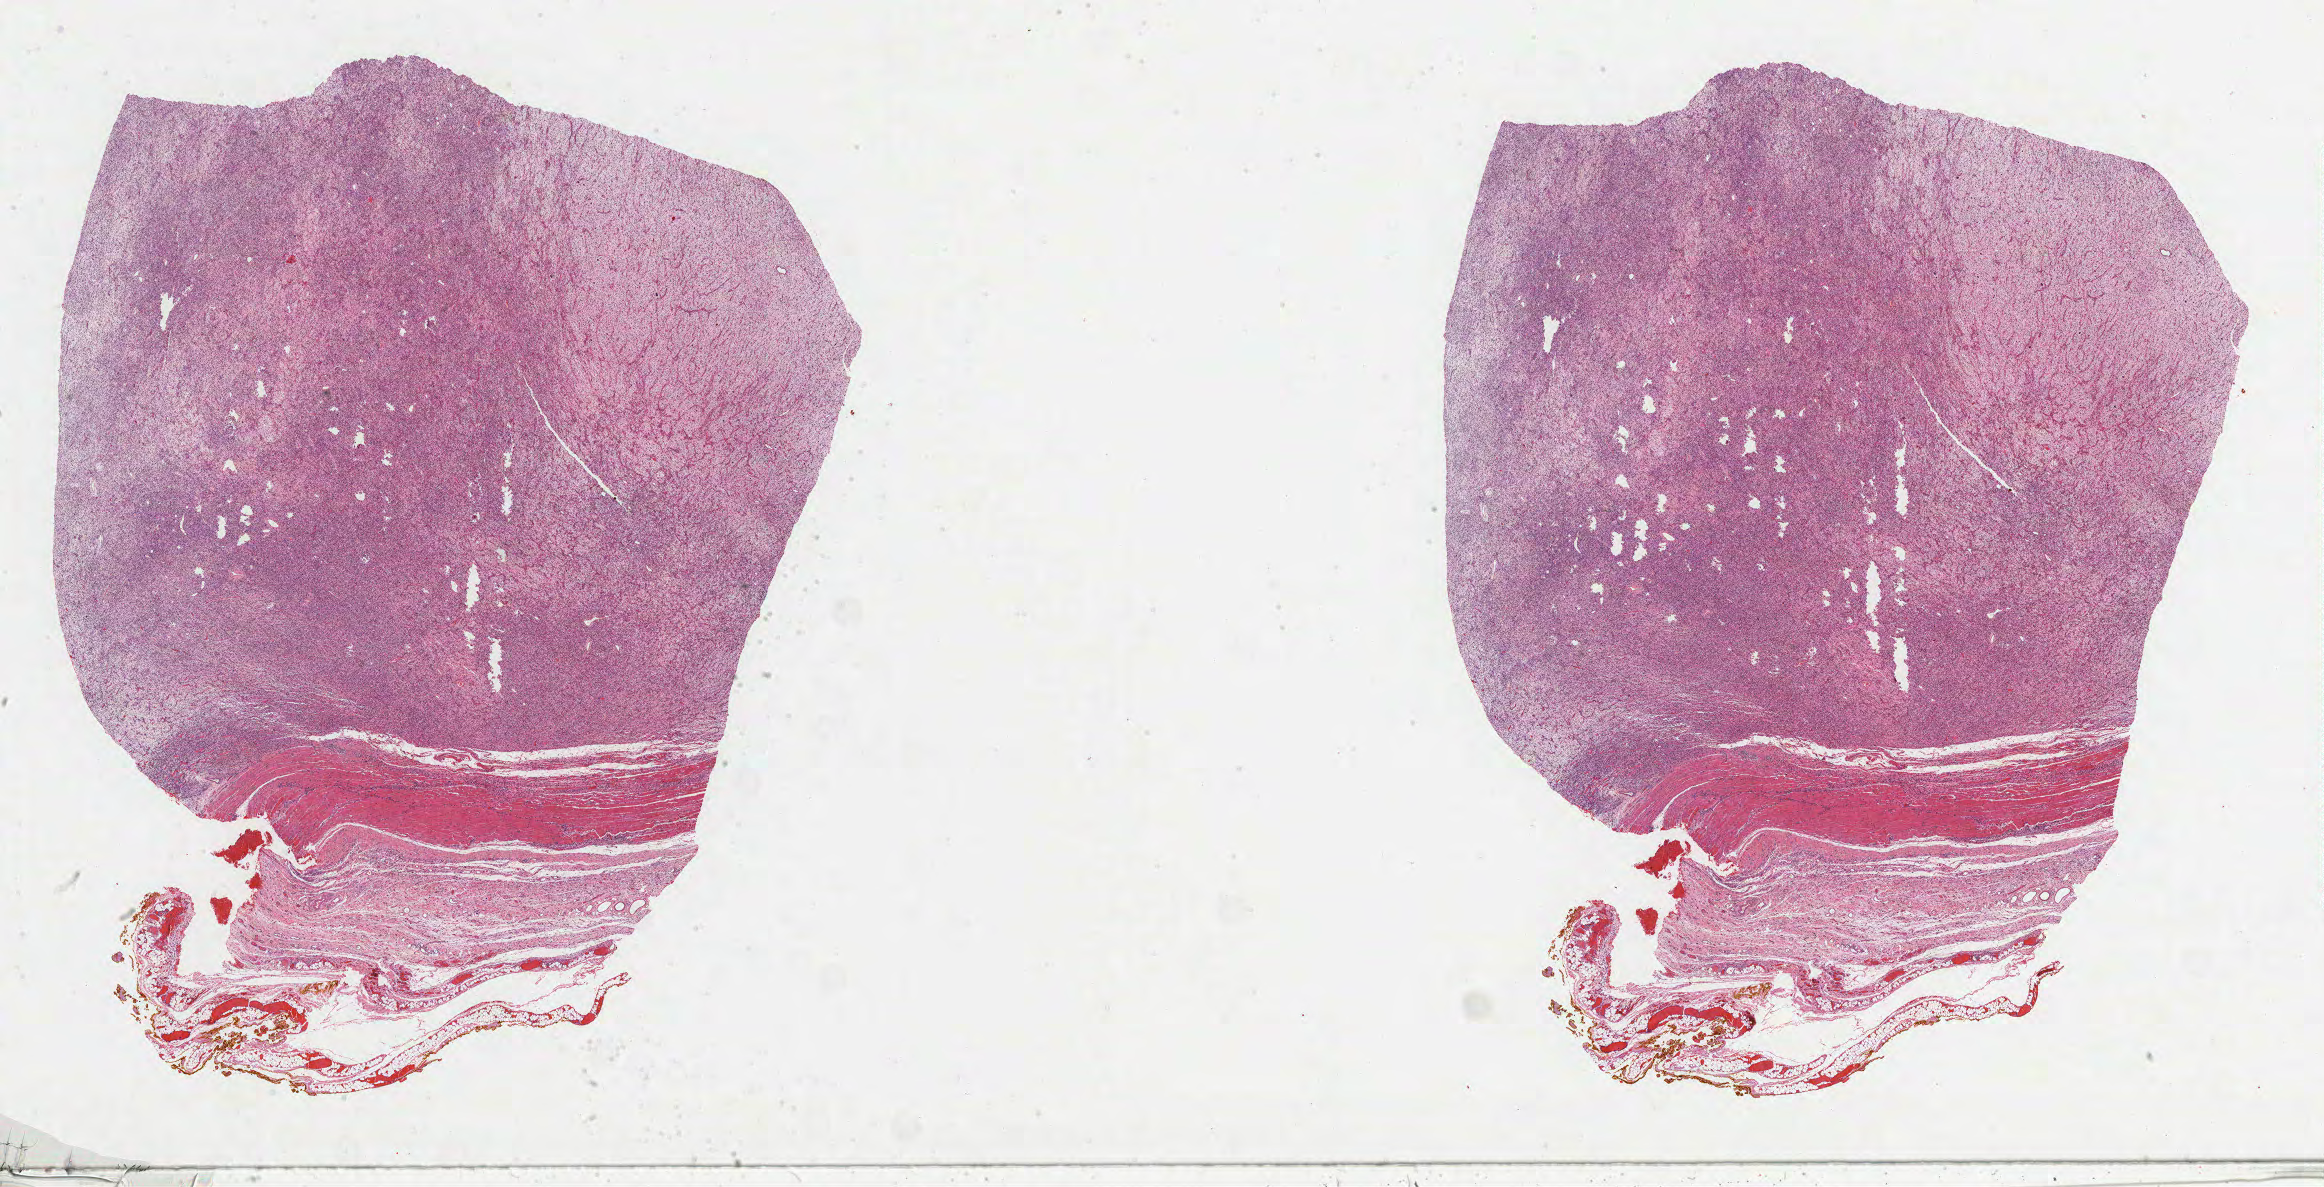
Whole-slide histology image, H&E-stained — whole scanned area (about 37.5 x 19.2 mm) shown as a low-resolution overview. Formalin-fixed paraffin-embedded (FFPE) diagnostic section. Primary tumour sample from the connective, subcutaneous and other soft tissues. Male patient; age at initial diagnosis 68 years.
Pathologic diagnosis: Dedifferentiated liposarcoma (connective, subcutaneous and other soft tissues of upper limb and shoulder).